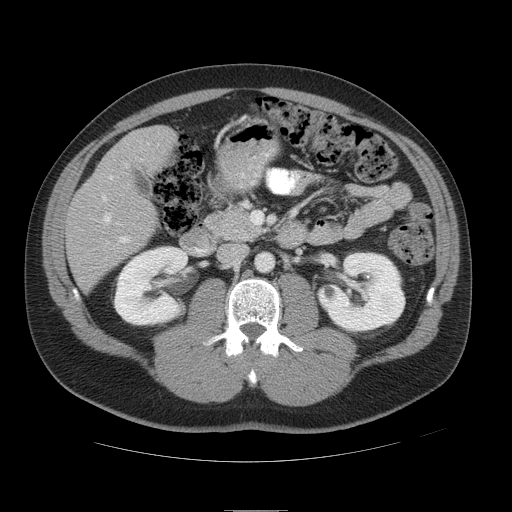
Contrast-enhanced abdominal CT, one axial slice; reconstruction kernel STANDARD; intravenous contrast given; soft-tissue window (W 400 / L 40 HU); 5 mm slice thickness; 512 × 512 image matrix, field of view 425 × 425 mm. Male patient, age 52 years. Case-level facts recorded for this patient, not image findings: diagnosis: colorectal cancer liver metastases, imaged before liver resection; multiple liver metastases: yes; largest metastasis: 5.1 cm; chemotherapy before resection: yes.
Annotated regions visible in this slice (expert manual segmentation):
- hepatic veins: bounding box <103,143,149,223> (left, top, right, bottom; pixels)
- liver: <67,126,175,288>
- planned liver remnant (the part of the liver to remain after resection): <133,126,175,159>
- portal vein (with intrahepatic branches): <101,175,131,243>